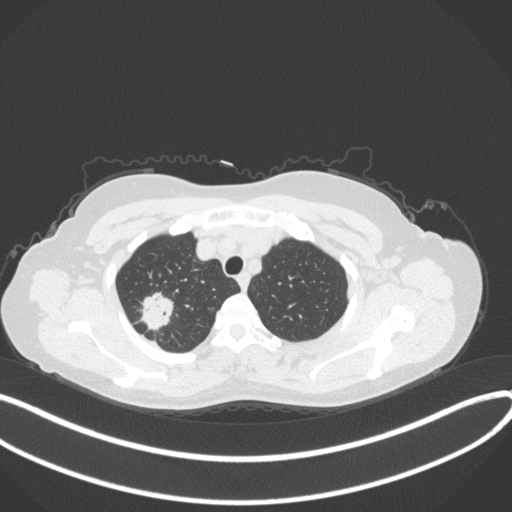
Chest CT, one axial slice; position 306 of 342 along the scan axis; reconstruction kernel B31f; 120 kVp; lung window (W 1500 / L -600 HU); 1 mm slice thickness; 512 × 512 image matrix. Female patient, age 50 years. From the clinical record (not read from this slice): clinical TNM (as recorded): T1c N0 M0; histopathological grade: G2-3.
Outlined on this slice (rectangle marked by the reading radiologist):
- lung tumour (recorded histology: adenocarcinoma): box from (x=136, y=291) to (x=180, y=334) px